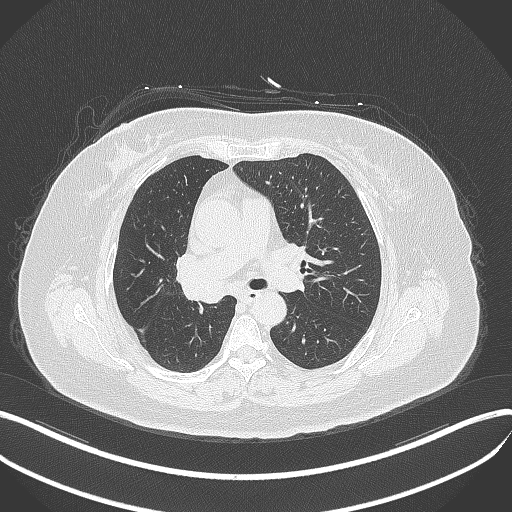
Chest CT, one axial slice. Slice 216 of 376 in the series (ordered by position). Reconstruction kernel B70f. Lung window (W 1500 / L -600 HU). 1 mm slice thickness. 512 × 512 image matrix, field of view 400 × 400 mm. Female patient, age 60 years. Case-level facts recorded for this patient, not image findings: clinical TNM (as recorded): T1c N0 M0; histopathological grade: G1-G2.
Annotated regions visible in this slice (bounding box drawn by a radiologist):
- lung tumour (recorded histology: squamous cell carcinoma): box from (x=180, y=271) to (x=230, y=309) px